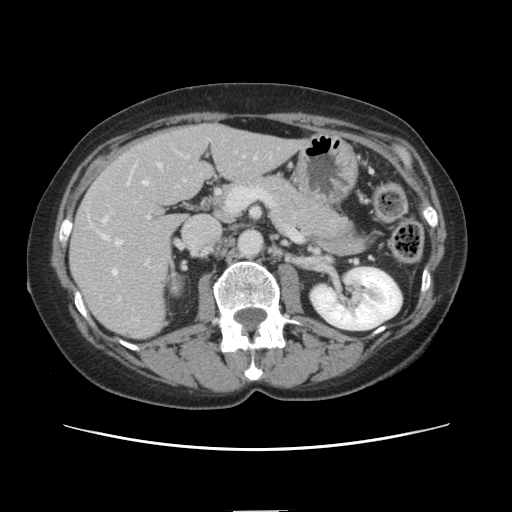
Contrast-enhanced abdominal CT, one axial slice; slice 64 of 141 in the series (ordered by position); intravenous contrast given; soft-tissue window (W 400 / L 40 HU); 2.5 mm slice thickness; 512 × 512 image matrix, field of view 350 × 350 mm. Female patient, age 63 years. From the clinical record (not read from this slice): diagnosis: colorectal cancer liver metastases, imaged before liver resection.
Annotated regions visible in this slice (outlined manually by an expert reader):
- hepatic veins: bounding box <104,164,161,276> (left, top, right, bottom; pixels)
- liver: <71,125,301,338>
- planned liver remnant (the part of the liver to remain after resection): <176,125,301,189>
- portal vein (with intrahepatic branches): <103,164,147,224>